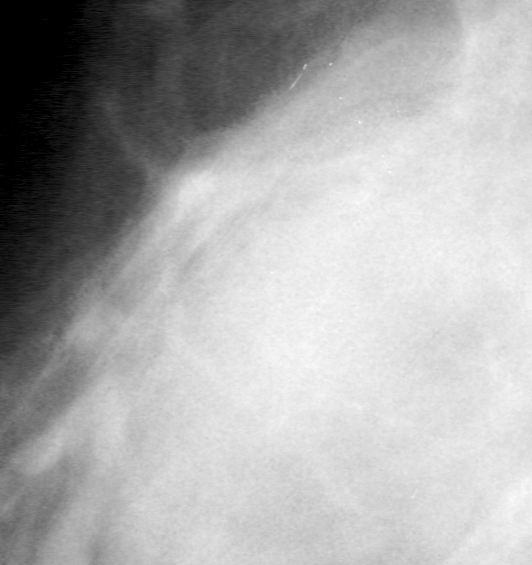
Cropped region of a digitized screen-film mammogram centred on a radiologist-marked abnormality; left breast; MLO view; BI-RADS breast density category 4 (scale 1–4).
- Mass, shape oval, margins obscured; BI-RADS assessment category 4; subtlety rating 4 on a 1 (subtle) to 5 (obvious) scale; pathology (as recorded): benign.